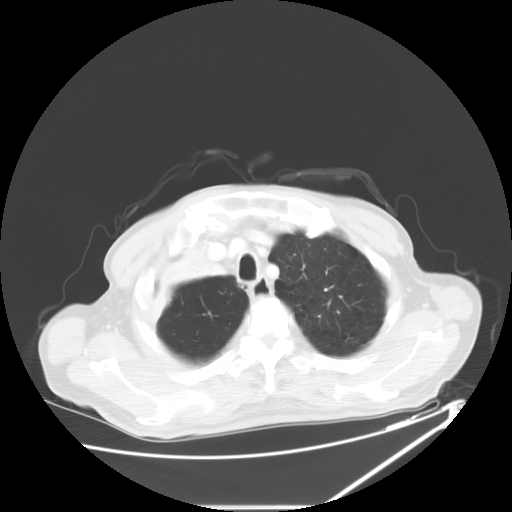
Chest CT, one axial slice; position 52 of 60 along the scan axis; reconstruction kernel STANDARD; lung window (W 1500 / L -600 HU); 5 mm slice thickness; 512 × 512 image matrix, field of view 410 × 410 mm. Patient: male, 73 years. From the clinical record (not read from this slice): clinical TNM (as recorded): T2a N1 M0.
Outlined on this slice (rectangle marked by the reading radiologist):
- lung tumour (recorded histology: squamous cell carcinoma): bounding box [x1, y1, x2, y2] px = [147, 225, 229, 328]